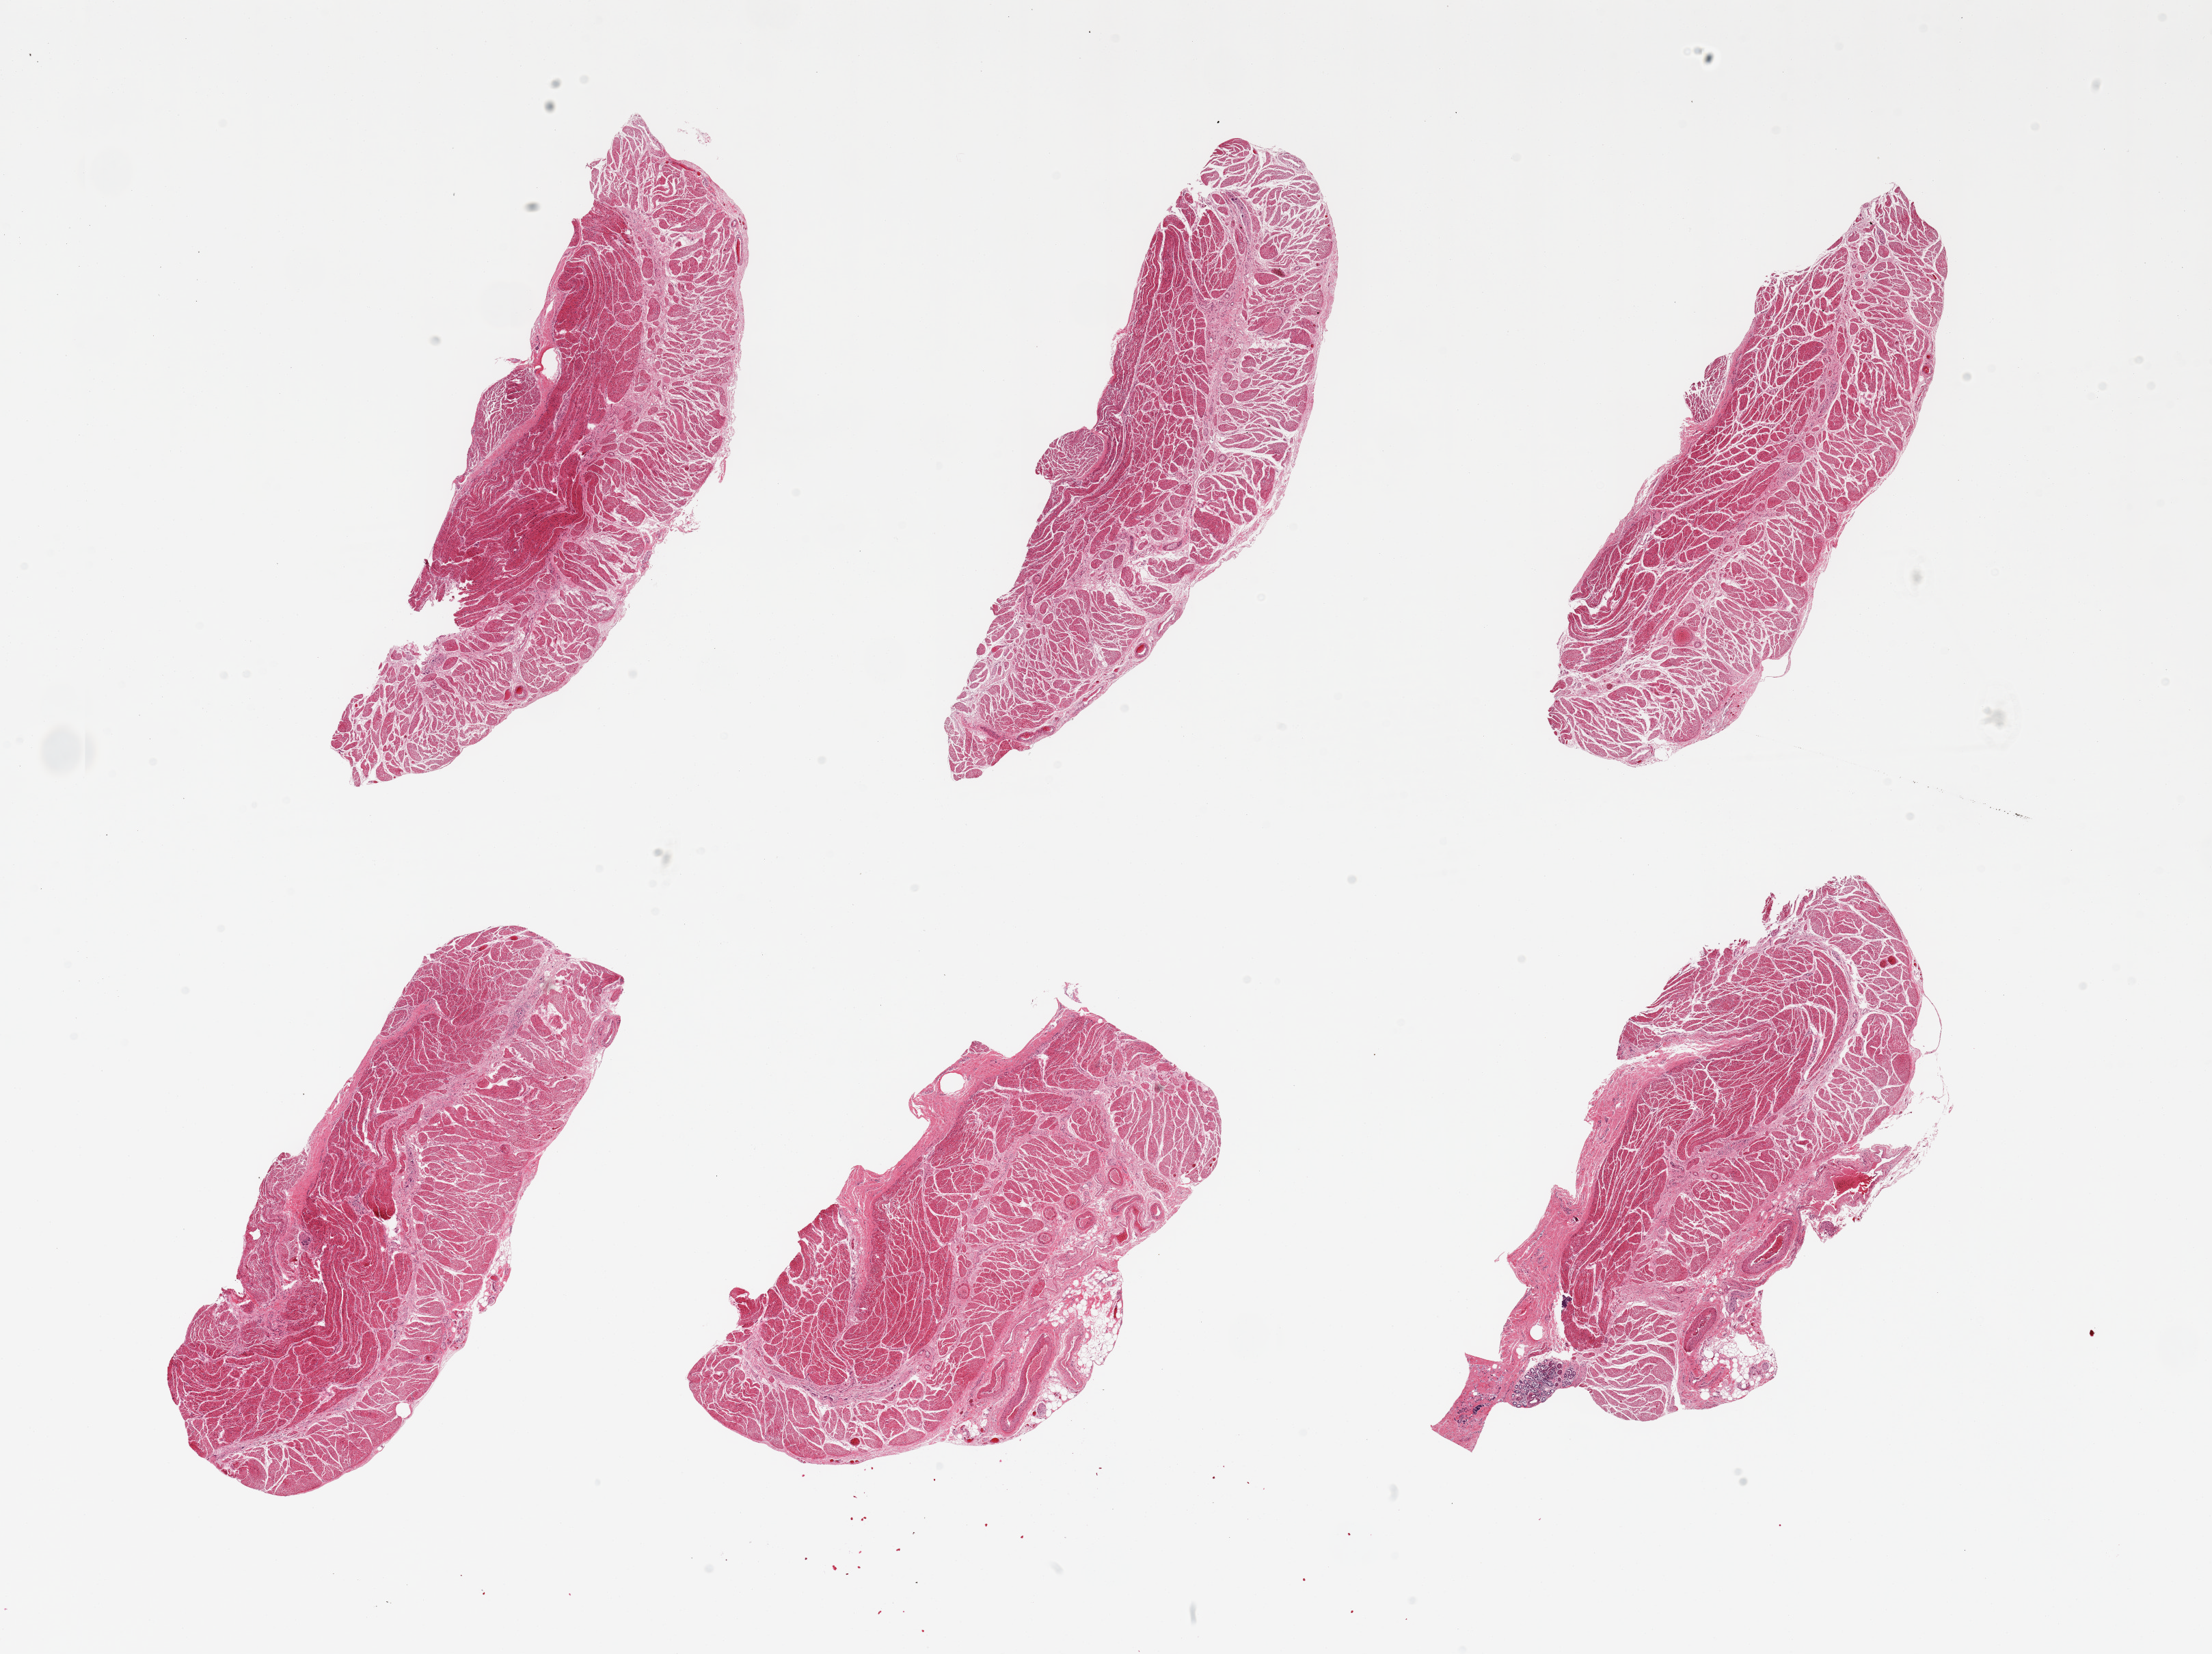
Digitized hematoxylin and eosin (H&E)-stained section, shown as a low-resolution overview of the whole scanned area (about 25.6 x 19.1 mm, slide scanned at 20x), PAXgene-fixed paraffin-embedded (PFPE) section, sampled site (target tissue): esophageal muscle, donor tissue sample. Donor sex: male.
Pathologist's review note for this sample: 6 pieces; predominantly muscularis with few larger vessels/nerve and focus of submucosal glands.